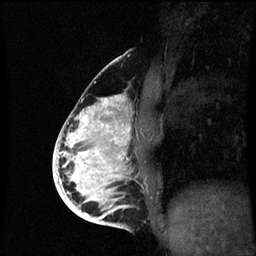
Breast MRI (dynamic contrast-enhanced), one sagittal slice. Position 30 of 60 along the scan axis. Dynamic contrast-enhanced series, image 2 of 3 at this slice position (ordered by acquisition). 1.5 T. TE 4.2 ms, TR 8.9 ms. 2 mm slice thickness. 256 × 256 image matrix, field of view 200 × 200 mm. Female patient, age 35 years. Case-level facts recorded for this patient, not image findings: setting: breast cancer imaged before/during neoadjuvant chemotherapy; receptor status: HR-positive, HER2-negative.
Annotated regions visible in this slice (semi-automatically segmented with operator editing):
- analysis volume of interest (the breast-tissue region the enhancement analysis was run in; not a lesion): bounding box <66,94,141,215> (left, top, right, bottom; pixels)
- tumour enhancement mask (voxels above the 70 % enhancement threshold inside the analysis volume of interest): <66,96,131,215>